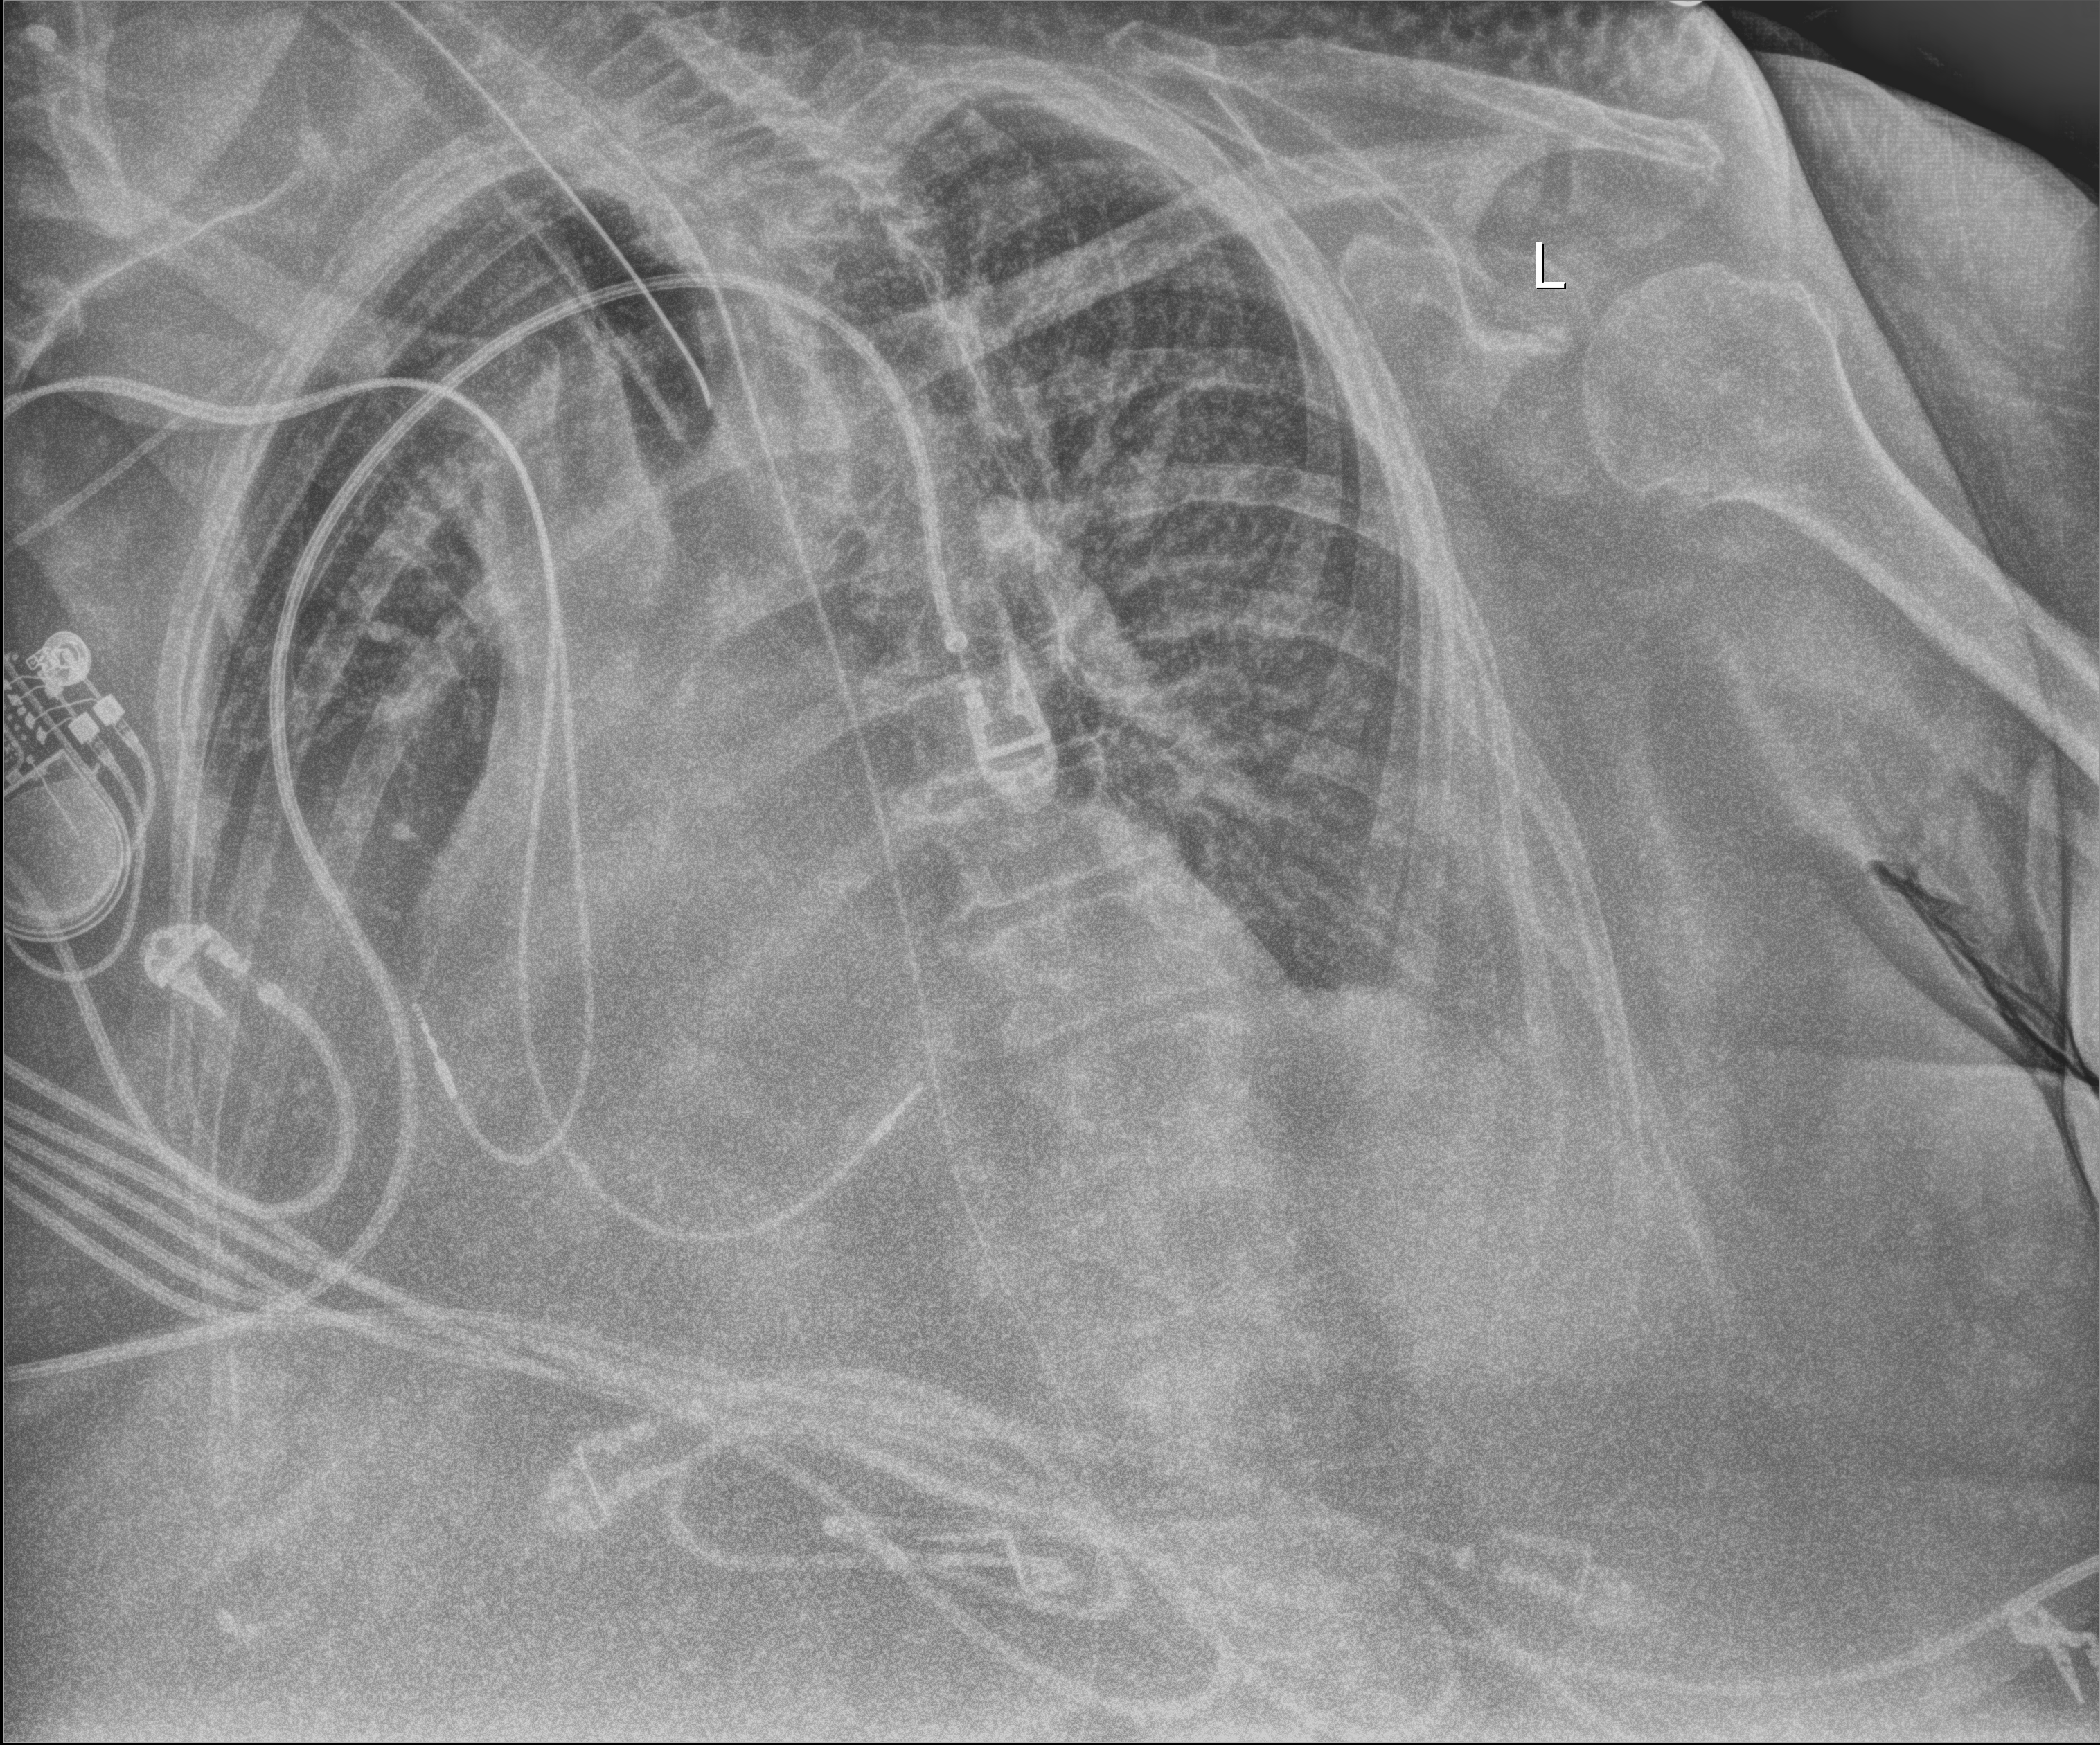
Chest X-ray (portable); anteroposterior (AP) projection. Female patient hospitalised with COVID-19, age 75–90 years.
Hospital-stay facts (about this admission, not read from this image; timing relative to this image not recorded): admitted to intensive care during this hospital stay: yes; mechanically ventilated during this hospital stay: yes.